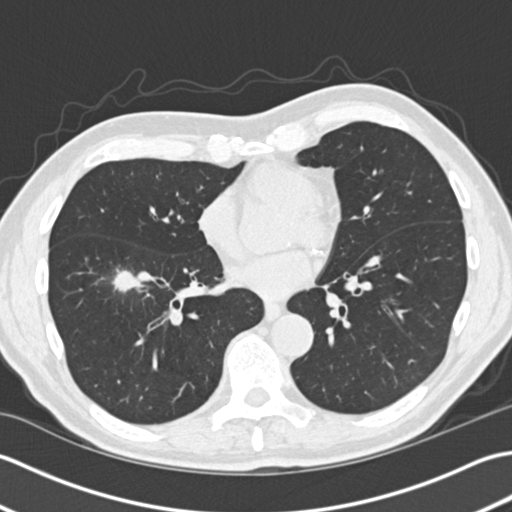
Axial slice from a low-dose chest CT screening exam. Second screening round (one year after baseline). Lung window (W 1500 / L -600 HU). 2 mm slice thickness. Standard (soft-tissue) reconstruction kernel (B30f). Male, age 73 years at enrolment. Former smoker at enrolment.
Expert-annotated lung lesion, bounding box <92,252,150,313> (left, top, right, bottom; pixels). Reader record for this screening exam (exam-level; its link to the box is not recorded): non-calcified nodule or mass ≥4 mm, right lower lobe, 18 × 15 mm, spiculated (stellate) margins, soft tissue attenuation, pre-existing on the prior screen: yes. Participant outcome: lung cancer diagnosed 87 days after this screen — non-small cell carcinoma, right lower lobe, stage IA (AJCC 6th edition), 30 mm at pathology.